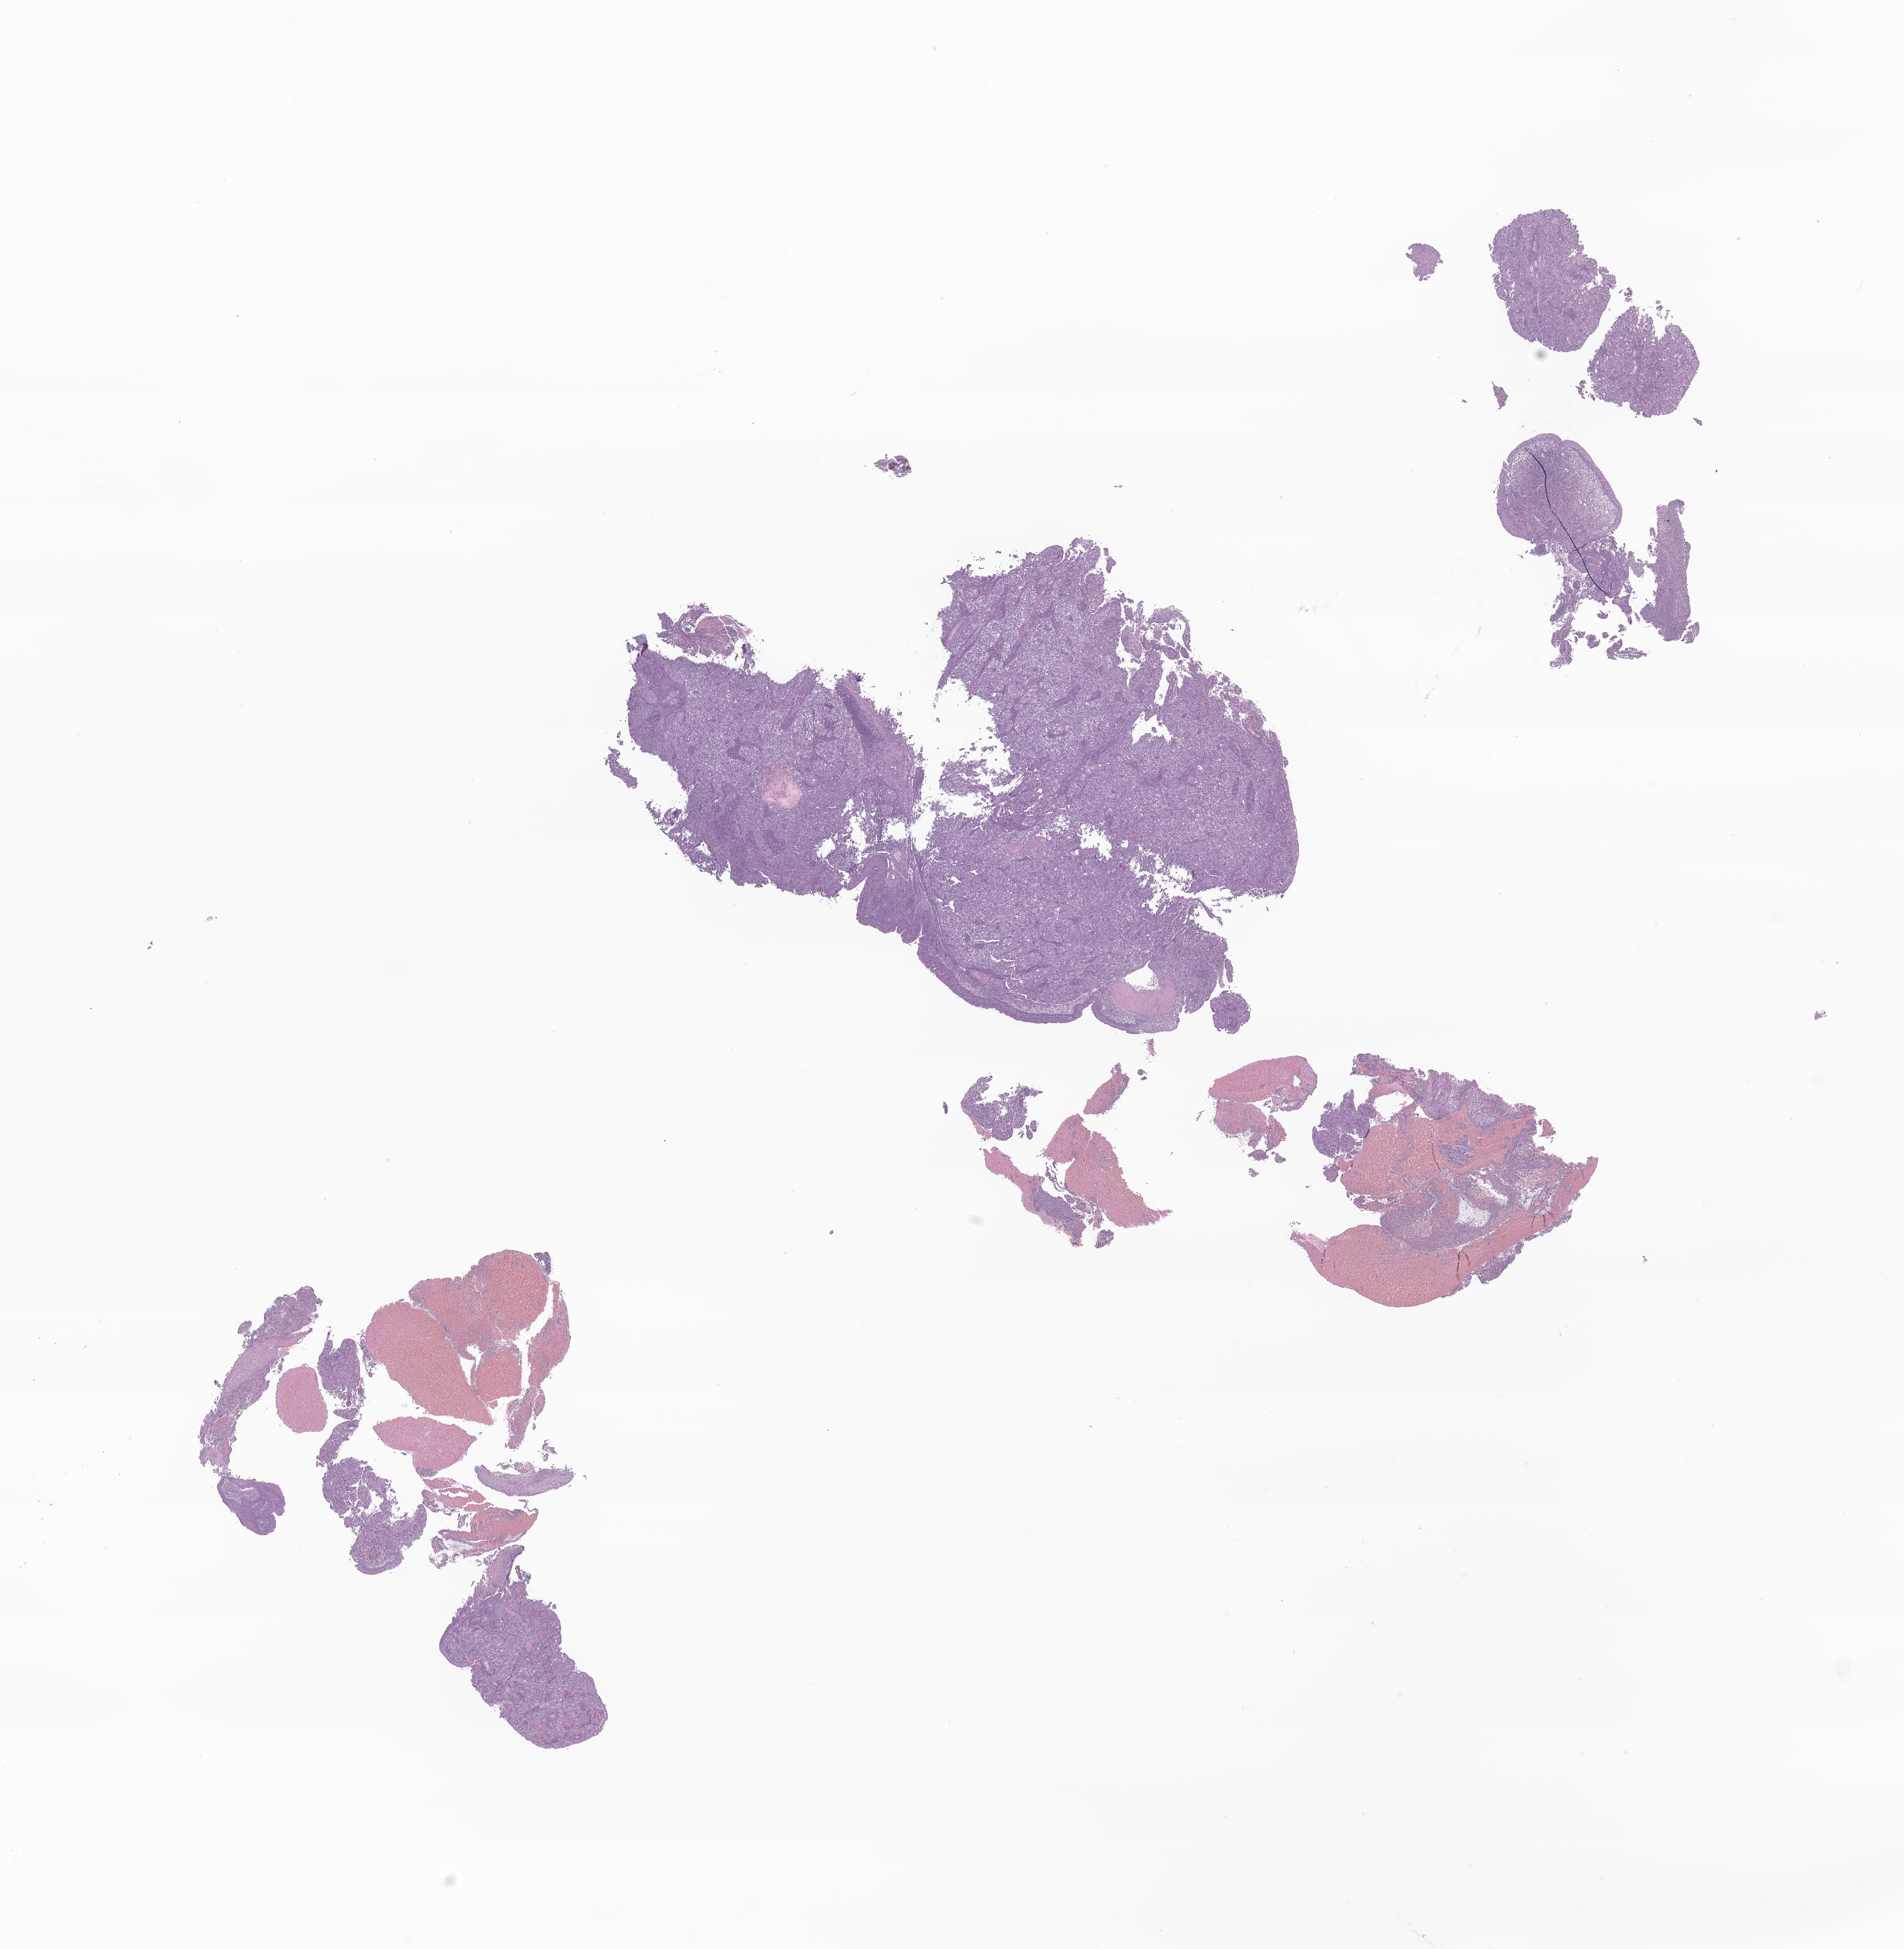
Digitized haematoxylin and eosin-stained section of tumor tissue from the lower lobe of lung, shown as a low-resolution overview of the whole scanned area (about 18.3 x 18.7 mm), formalin-fixed paraffin-embedded section. Male patient, age 250 months (20 years 10 months).
- tissue or organ of origin (case record): lower lobe, lung
- recorded diagnosis: Clear cell adenocarcinoma, NOS